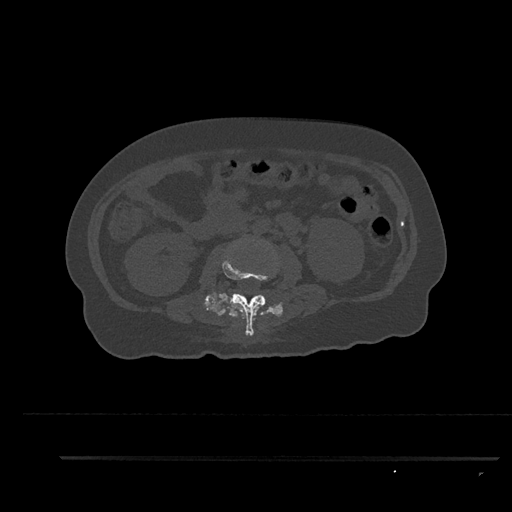
CT including the spine, one axial slice. Slice 133 of 797 in the series (ordered by position). Reconstruction kernel Br40s/3. 120 kVp. Bone window (W 1800 / L 400 HU). 512 × 512 image matrix. Patient: female, 44 years. From the clinical record (not read from this slice): primary cancer: renal.
Structures marked on this image (semi-automatic segmentation, software-assisted and operator-edited):
- L2 vertebra: bounding box [x1, y1, x2, y2] px = [222, 258, 268, 336]
- L3 vertebra: [265, 298, 266, 302]